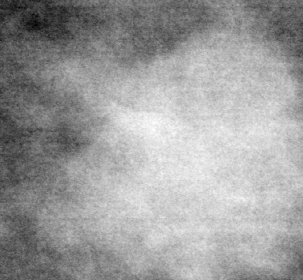
Cropped region of a digitized screen-film mammogram centred on a radiologist-marked abnormality, left breast, MLO view.
Mass, shape lobulated, margins ill defined; BI-RADS assessment category 4; pathology (as recorded): malignant.